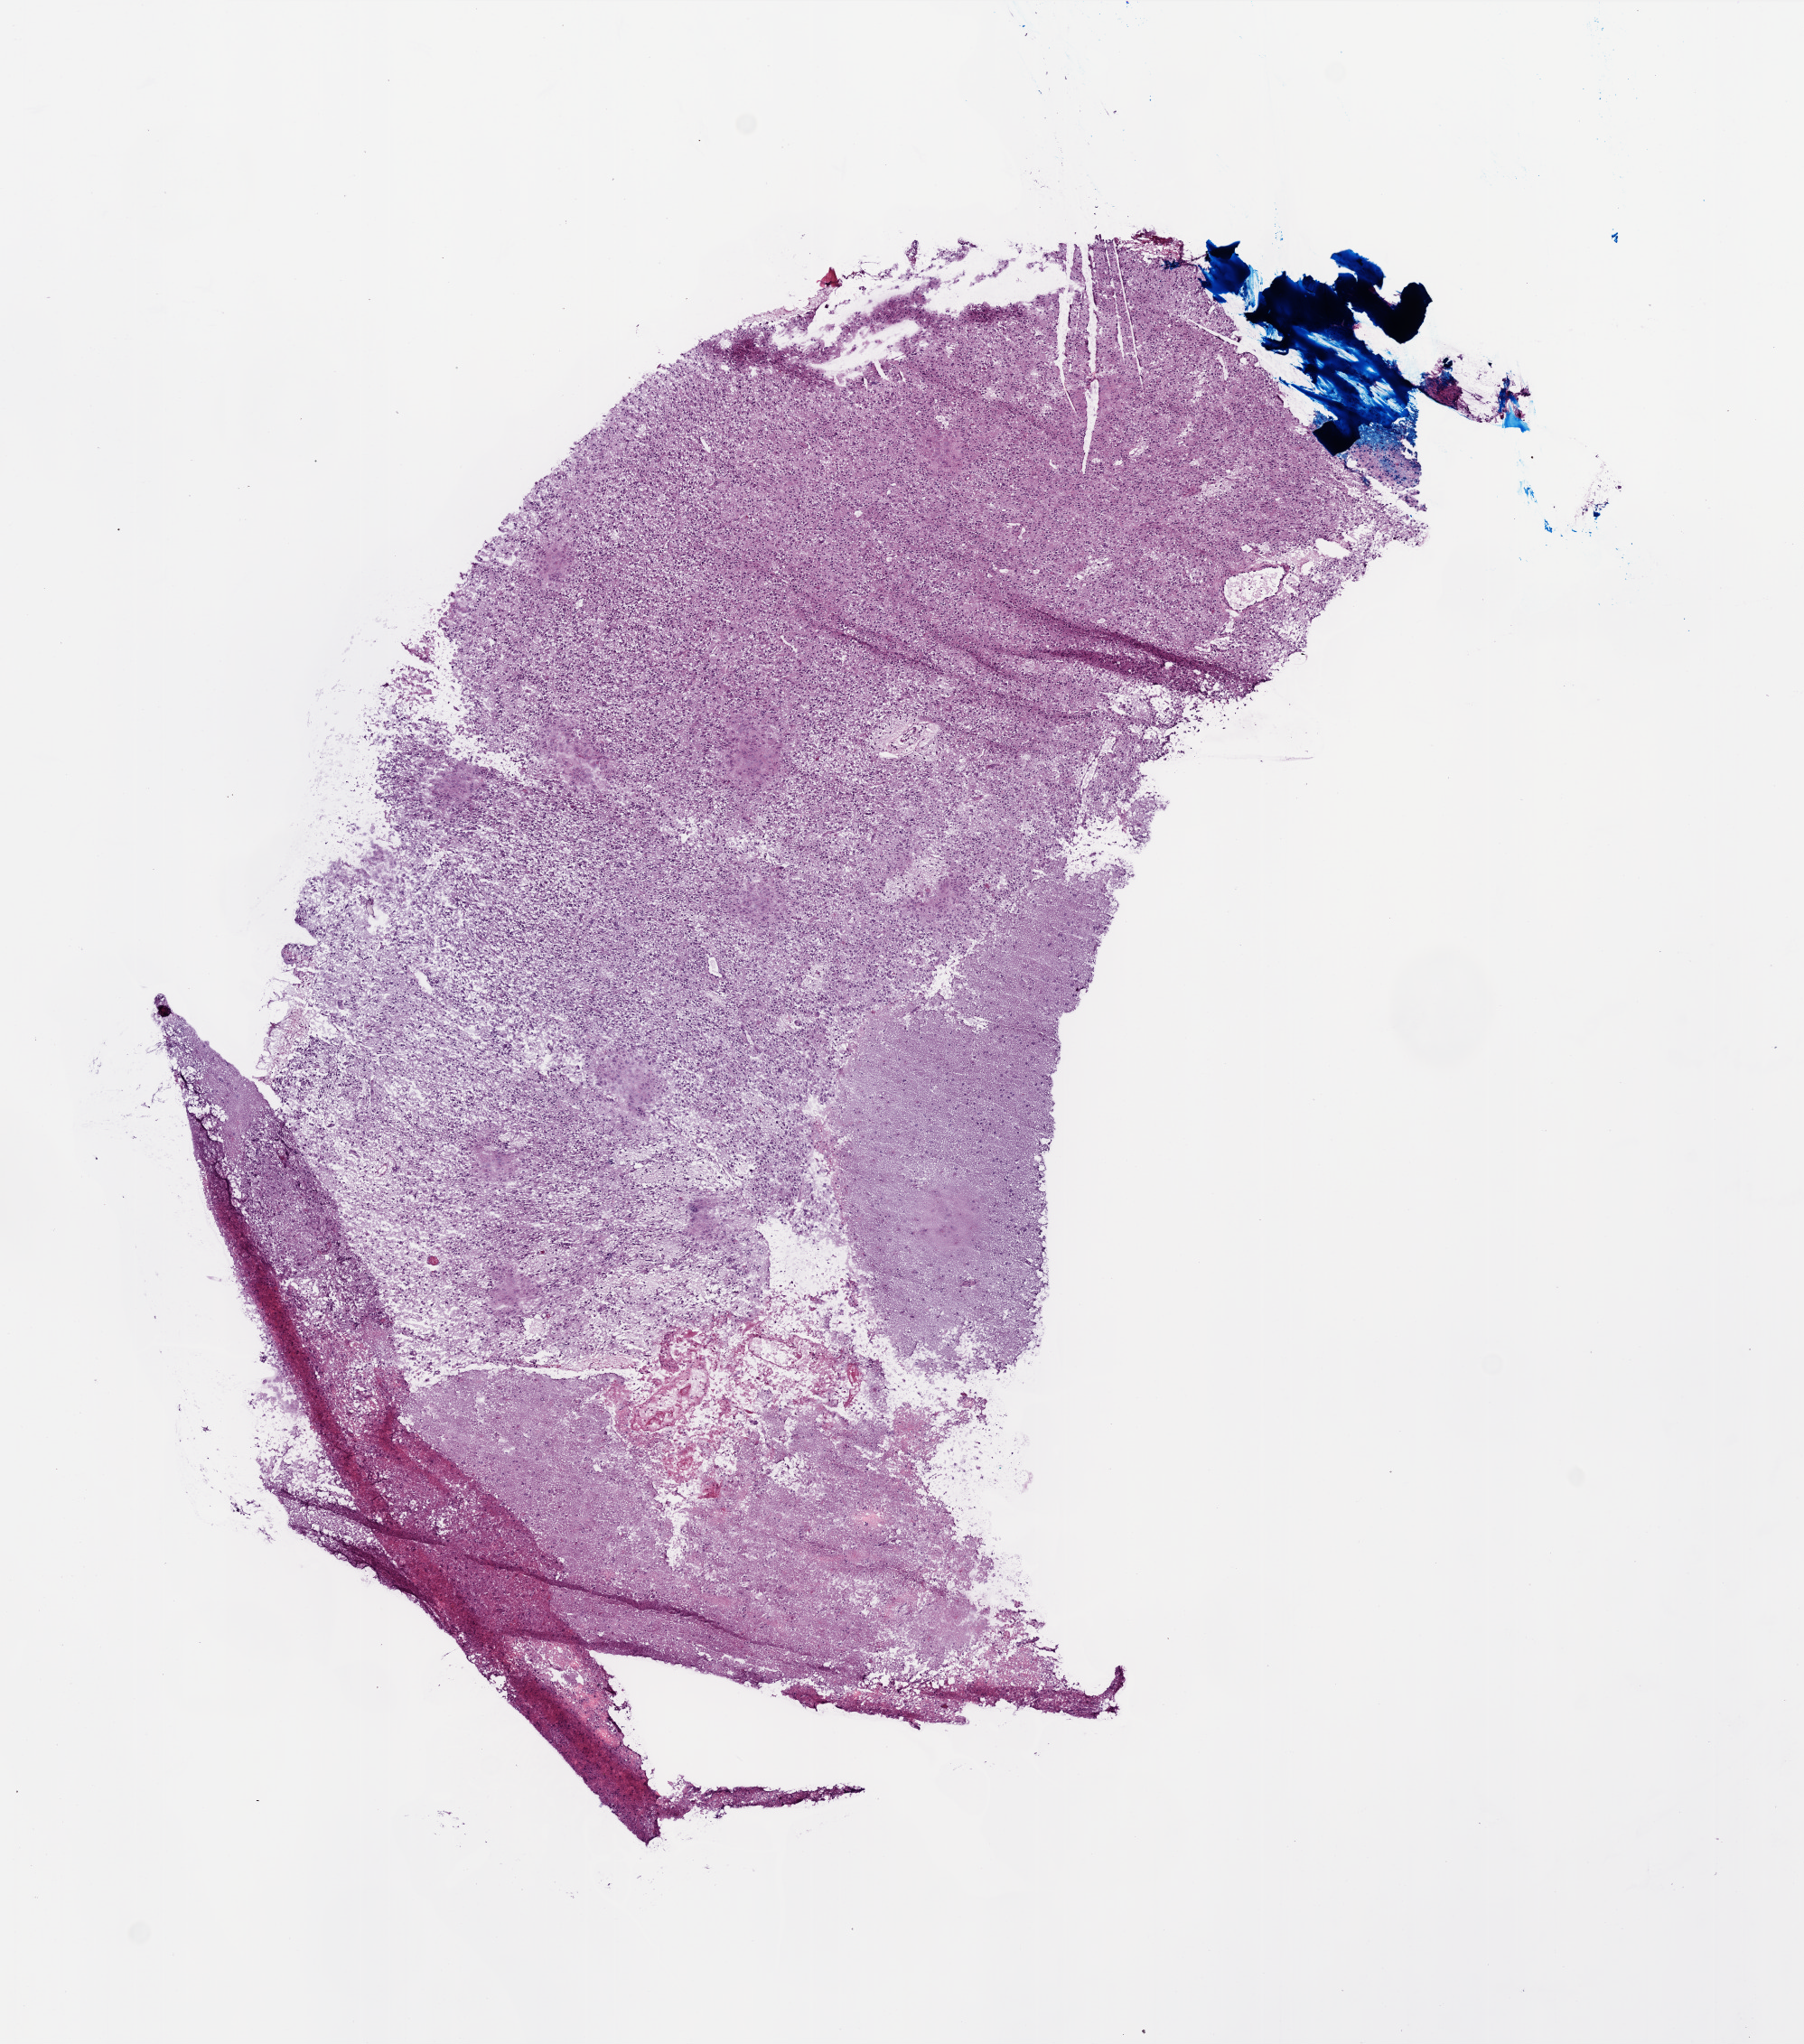
Whole-slide histology image, H&E — whole scanned area (about 8.0 x 9.1 mm) shown as a low-resolution overview. Frozen section. Brain, primary tumour sample. Male, age 30 years at initial diagnosis. Slide review estimates, as recorded: tumour cells 80%, tumour nuclei 90%, normal cells 10%, stromal cells 0%, necrosis 10%.
Pathologic diagnosis: Glioblastoma.